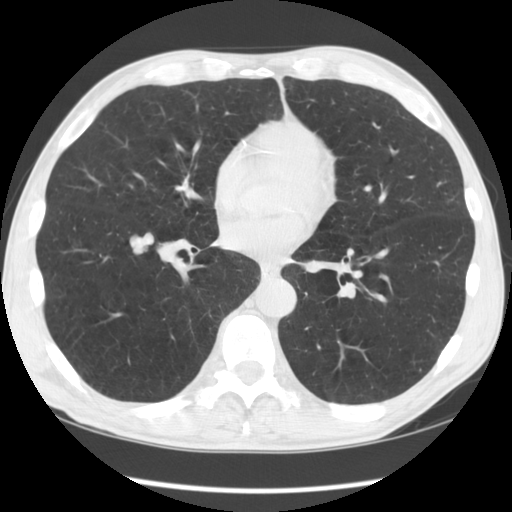
Low-dose screening chest CT, axial slice, second annual screen, lung window (W 1500 / L -600 HU), 2.5 mm slice thickness, standard (soft-tissue) reconstruction kernel (STANDARD), 512 × 512 image matrix. Male, age 60 years at enrolment. Current smoker at enrolment.
• Expert reader's lesion annotation, bounding box (x1, y1, x2, y2) in pixels: (111, 228, 162, 268).
• The exam's reader record, not a measurement of the box and not confirmed to be the same lesion: non-calcified nodule or mass ≥4 mm, right lower lobe, 17 × 14 mm, smooth margins, soft tissue attenuation, pre-existing on the prior screen: yes; interval growth: yes.
• Participant outcome: lung cancer diagnosed 39 days after this screen — large cell carcinoma, NOS, right lower lobe, undifferentiated (G4), stage IA (AJCC 6th edition), 16 mm at pathology.